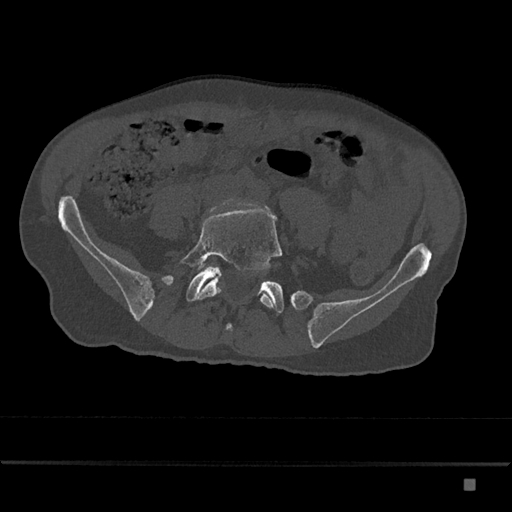
CT including the spine, one axial slice; slice 266 of 797 in the series (ordered by position); bone window (W 1800 / L 400 HU); 0.5 mm slice thickness; 512 × 512 image matrix, field of view 390 × 390 mm. Patient: male, 72 years. Case-level facts recorded for this patient, not image findings: primary cancer: prostate.
Structures marked on this image (semi-automatic segmentation, software-assisted and operator-edited):
- L5 vertebra: bounding box <180,209,283,308> (left, top, right, bottom; pixels)